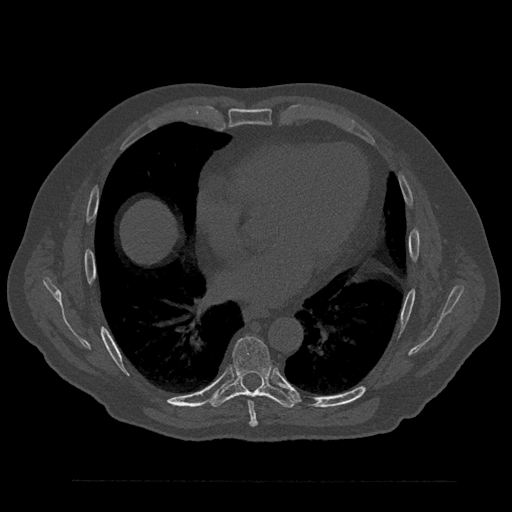
CT including the spine, one axial slice. Position 470 of 797 along the scan axis. 120 kVp. Bone window (W 1800 / L 400 HU). 512 × 512 image matrix. Patient: male, 61 years. From the clinical record (not read from this slice): primary cancer: prostate.
Annotated regions visible in this slice (semi-automatically segmented with operator editing):
- T7 vertebra: bounding box <248,401,258,427> (left, top, right, bottom; pixels)
- T8 vertebra: <211,336,296,408>